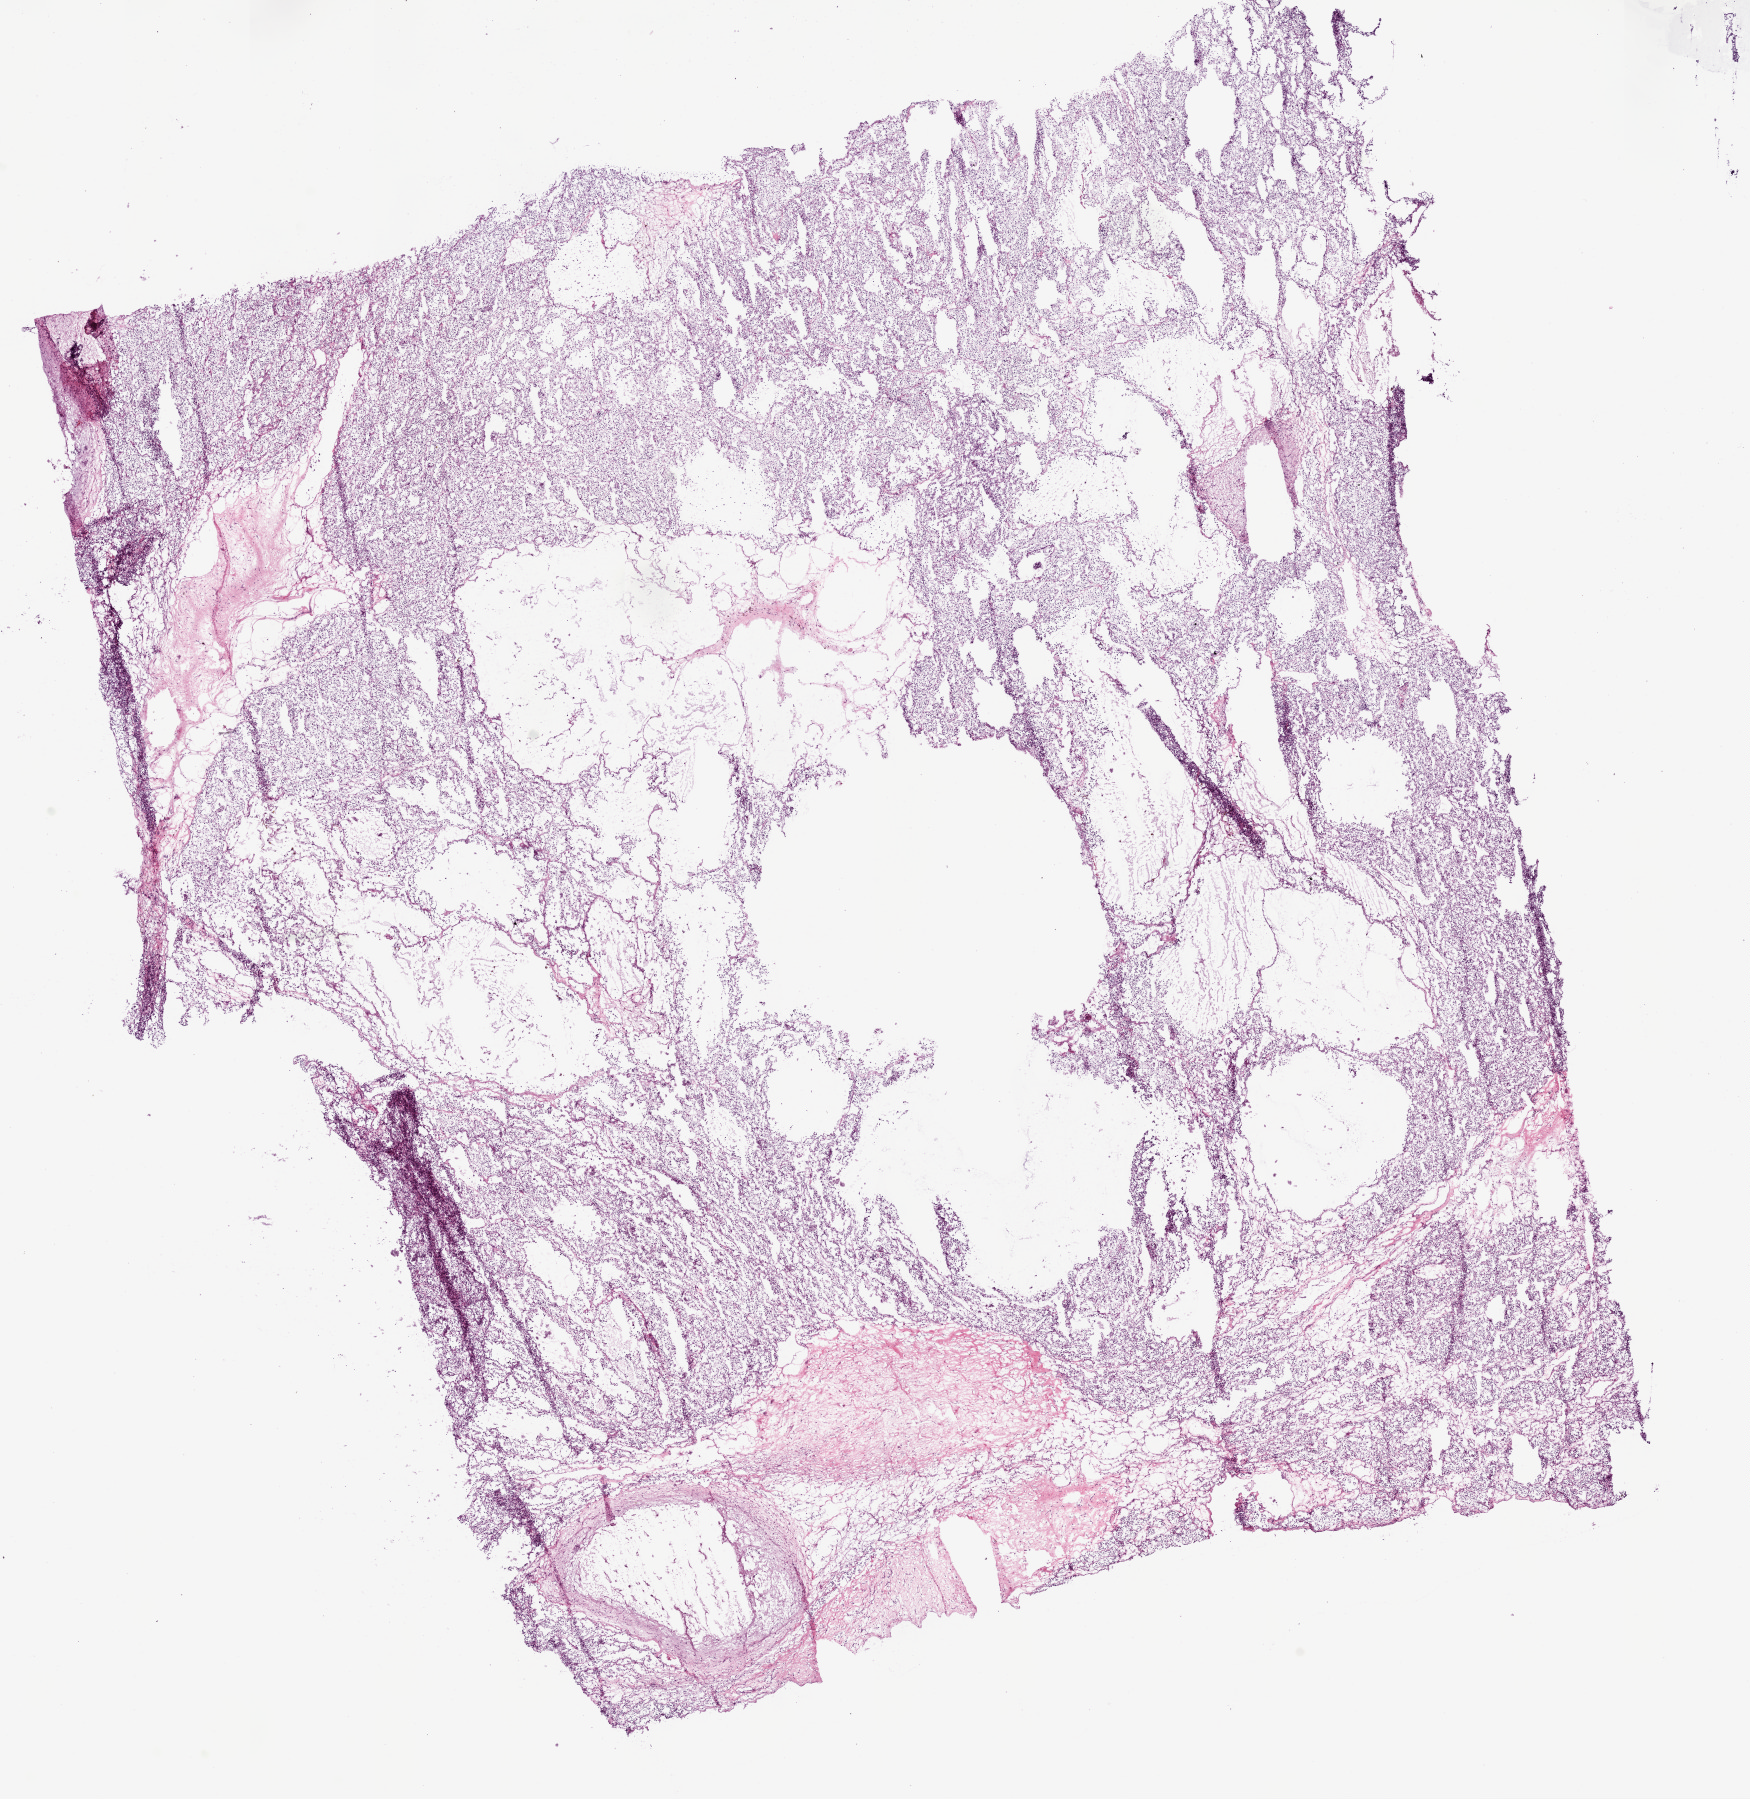
Whole-slide histology image, Hematoxylin and eosin (H&E) stained — low-resolution overview of the scanned area, about 14.0 x 14.4 mm (acquisition: 20x scan); frozen section from the bottom of the tissue portion; sample: primary tumour, kidney. Male, age 63 years at initial diagnosis. Histologic grade: G2 (moderately differentiated). Composition of this section per pathologist review: tumour cells 90%, tumour nuclei 90%, normal cells 0%, stromal cells 10%, necrosis 0%. Infiltration values recorded for this section: lymphocyte infiltration 2%, monocyte infiltration 0%, neutrophil infiltration 0%.
- TNM: T2 N0 M1
- AJCC pathologic stage: IV
- lymph nodes positive (case pathology): 0 of 3 examined
- pathologic diagnosis: Clear cell adenocarcinoma, NOS
- laterality: right